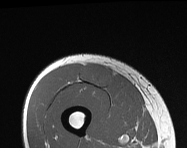
MRI of an extremity soft-tissue mass, one axial slice; position 45 of 114 along the scan axis; MR volume resampled by the dataset authors to the PET/CT grid (not the native acquisition matrix); 3.27 mm slice thickness; 187 × 148 image matrix, field of view 183 × 145 mm. Male patient. Case-level facts recorded for this patient, not image findings: histological type: pleiomorphic leiomyosarcoma; grade: intermediate; site of the primary tumour: right thigh.
Outlined on this slice (expert contour drawn on MRI and transferred to this co-registered scan by the dataset authors):
- gross tumour volume including surrounding oedema: box from (x=80, y=63) to (x=113, y=87) px